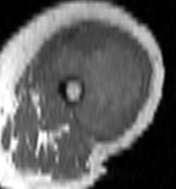
MRI of an extremity soft-tissue mass, one axial slice; slice 51 of 100 in the series (ordered by position); MR volume resampled by the dataset authors to the PET/CT grid (not the native acquisition matrix); 176 × 189 image matrix, field of view 172 × 185 mm. Female patient. Case-level facts recorded for this patient, not image findings: histological type: undifferentiated – high grade; grade: high; site of the primary tumour: left thigh.
Structures marked on this image (expert contour drawn on MRI and transferred to this co-registered scan by the dataset authors):
- gross tumour volume including surrounding oedema: bounding box (x1, y1, x2, y2) in pixels: (50, 25, 145, 142)
- gross tumour volume (mass): (50, 25, 145, 142)